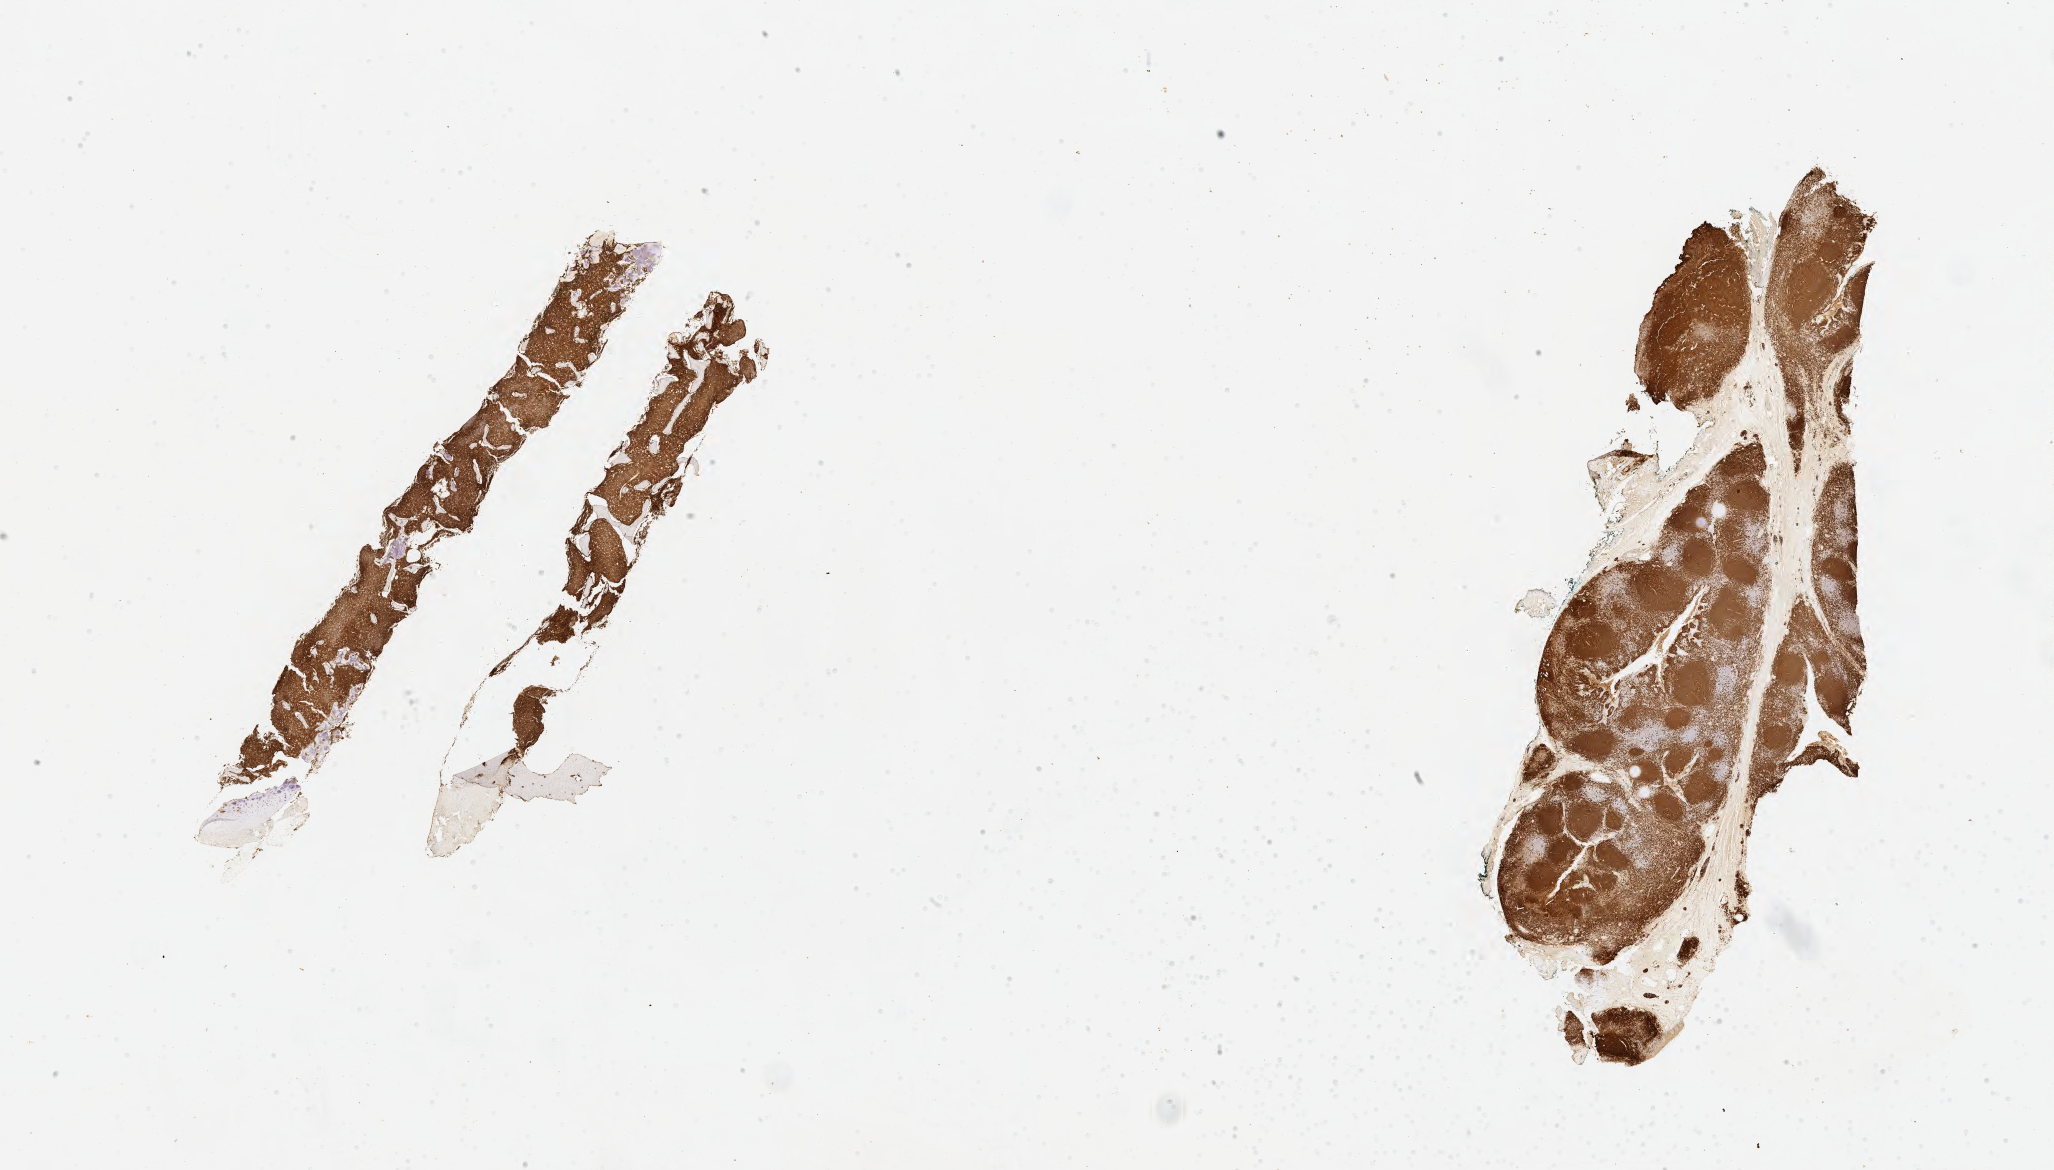
IHC for CD20, whole-slide image, shown as a low-resolution overview of the whole scanned area (about 33.2 x 18.9 mm), tumor tissue, anatomic site: bone marrow. Patient: male, 16 years old.
• diagnosis: Burkitt lymphoma, NOS